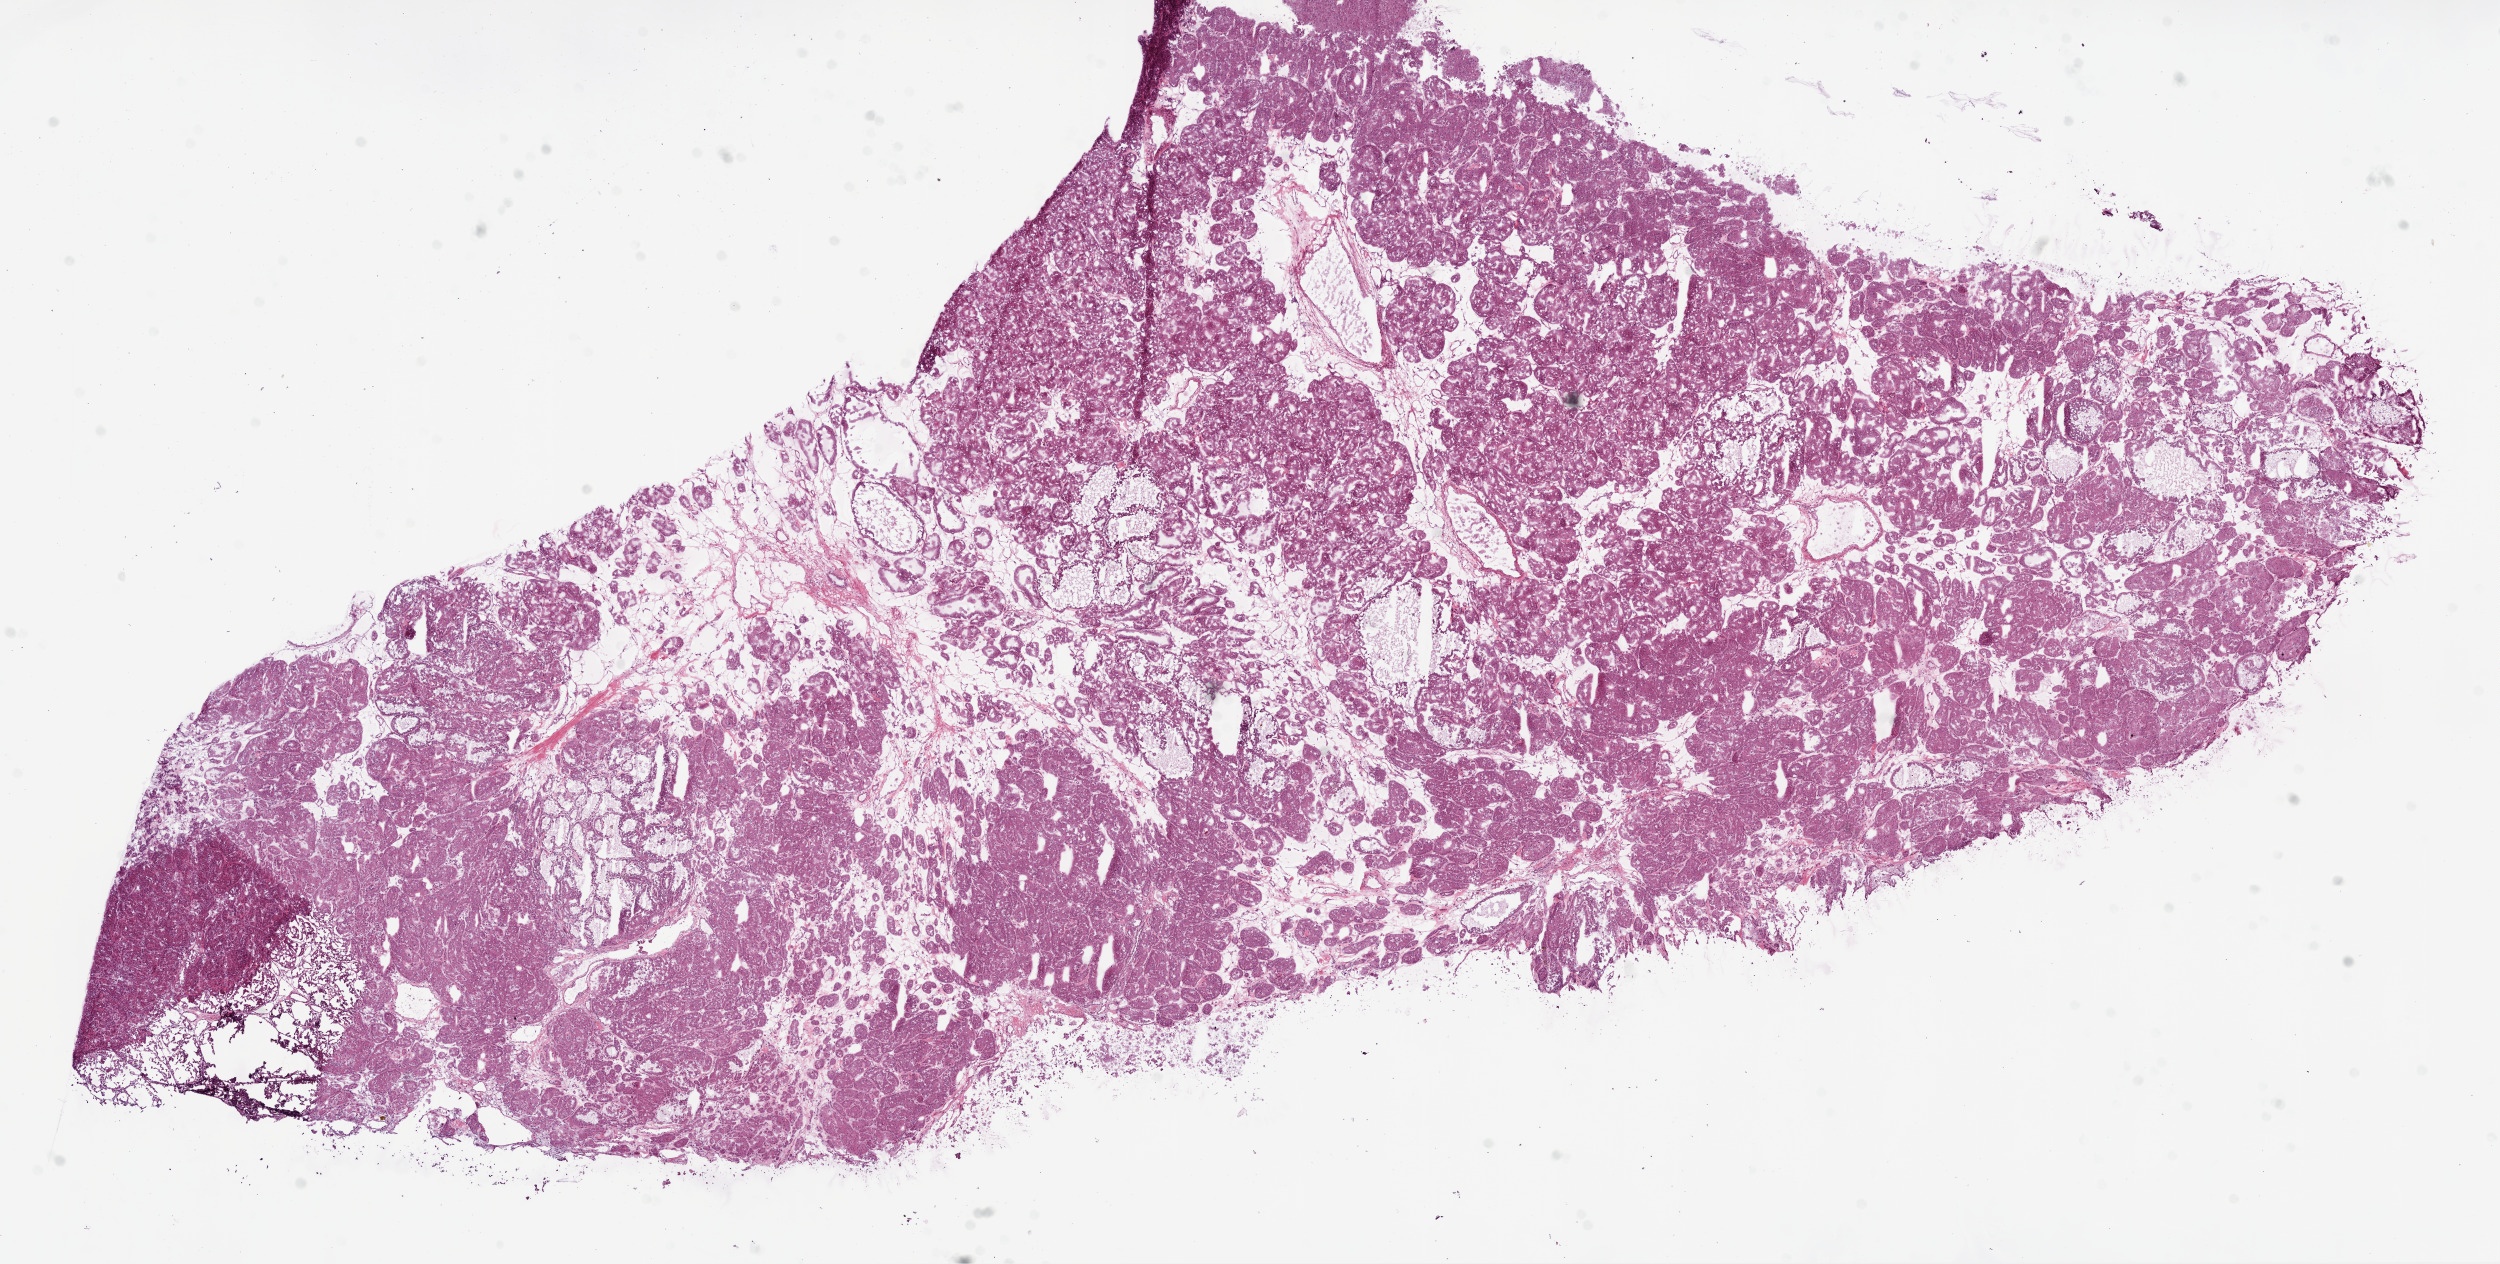
Digitized H&E tissue section (whole slide) — low-resolution overview of the scanned area, about 20.1 x 10.1 mm; frozen section from the bottom of the tissue portion; sample: primary tumour, kidney. Male, age 49 years at initial diagnosis. Histologic grade: G3 (poorly differentiated). Pathologist review of this section (percent, as recorded): tumour cells 80%, tumour nuclei 85%, normal cells 0%, stromal cells 20%, necrosis 0%.
TNM: T1a N0 M0. AJCC pathologic stage: I. Diagnosis: Clear cell adenocarcinoma, NOS.